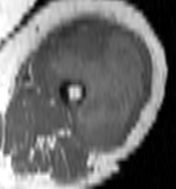
MRI of an extremity soft-tissue mass, one axial slice; slice 59 of 100 in the series (ordered by position); MR volume resampled by the dataset authors to the PET/CT grid (not the native acquisition matrix); 176 × 189 image matrix. Female patient. From the clinical record (not read from this slice): histological type: undifferentiated – high grade; grade: high; site of the primary tumour: left thigh.
Annotated regions visible in this slice (expert contour drawn on MRI and transferred to this co-registered scan by the dataset authors):
- gross tumour volume including surrounding oedema: bounding box [x1, y1, x2, y2] px = [46, 23, 145, 149]
- gross tumour volume (mass): [46, 23, 145, 149]